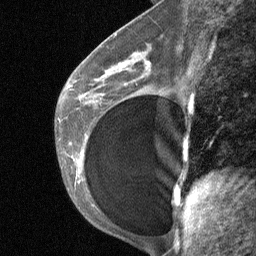
Breast MRI (dynamic contrast-enhanced), one sagittal slice. Position 38 of 64 along the scan axis. Dynamic contrast-enhanced study with each time point stored as its own series, time point 2 of 3 at this slice position (early post-contrast, ordered by acquisition time). 1.5 T. TE 4.8 ms, TR 27 ms. 2 mm slice thickness. 256 × 256 image matrix, field of view 180 × 180 mm. Female patient, age 35 years. From the clinical record (not read from this slice): setting: breast cancer imaged before/during neoadjuvant chemotherapy; receptor status: HR-positive, HER2-negative.
Annotated regions visible in this slice (semi-automatically segmented with operator editing):
- analysis volume of interest (the breast-tissue region the enhancement analysis was run in; not a lesion): bounding box [x1, y1, x2, y2] px = [74, 58, 164, 171]
- tumour enhancement mask (voxels above the 90 % enhancement threshold inside the analysis volume of interest): [106, 65, 124, 73]